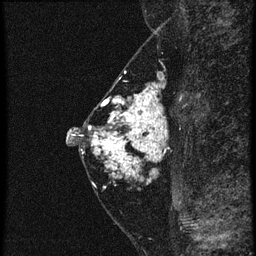
Breast MRI (dynamic contrast-enhanced), one sagittal slice; slice 27 of 60 in the series (ordered by position); 4 images stored at this slice position (order not interpretable as contrast timing); 1.5 T; TE 4.2 ms, TR 20.4 ms; 1.5 mm slice thickness; 256 × 256 image matrix, field of view 180 × 180 mm. Patient: female, 46 years. From the clinical record (not read from this slice): setting: breast cancer imaged before/during neoadjuvant chemotherapy; receptor status: triple-negative.
Annotated regions visible in this slice (semi-automatically segmented with operator editing):
- analysis volume of interest (the breast-tissue region the enhancement analysis was run in; not a lesion): bounding box [x1, y1, x2, y2] px = [88, 82, 171, 185]
- tumour enhancement mask (voxels above the 90 % enhancement threshold inside the analysis volume of interest): [90, 84, 165, 177]